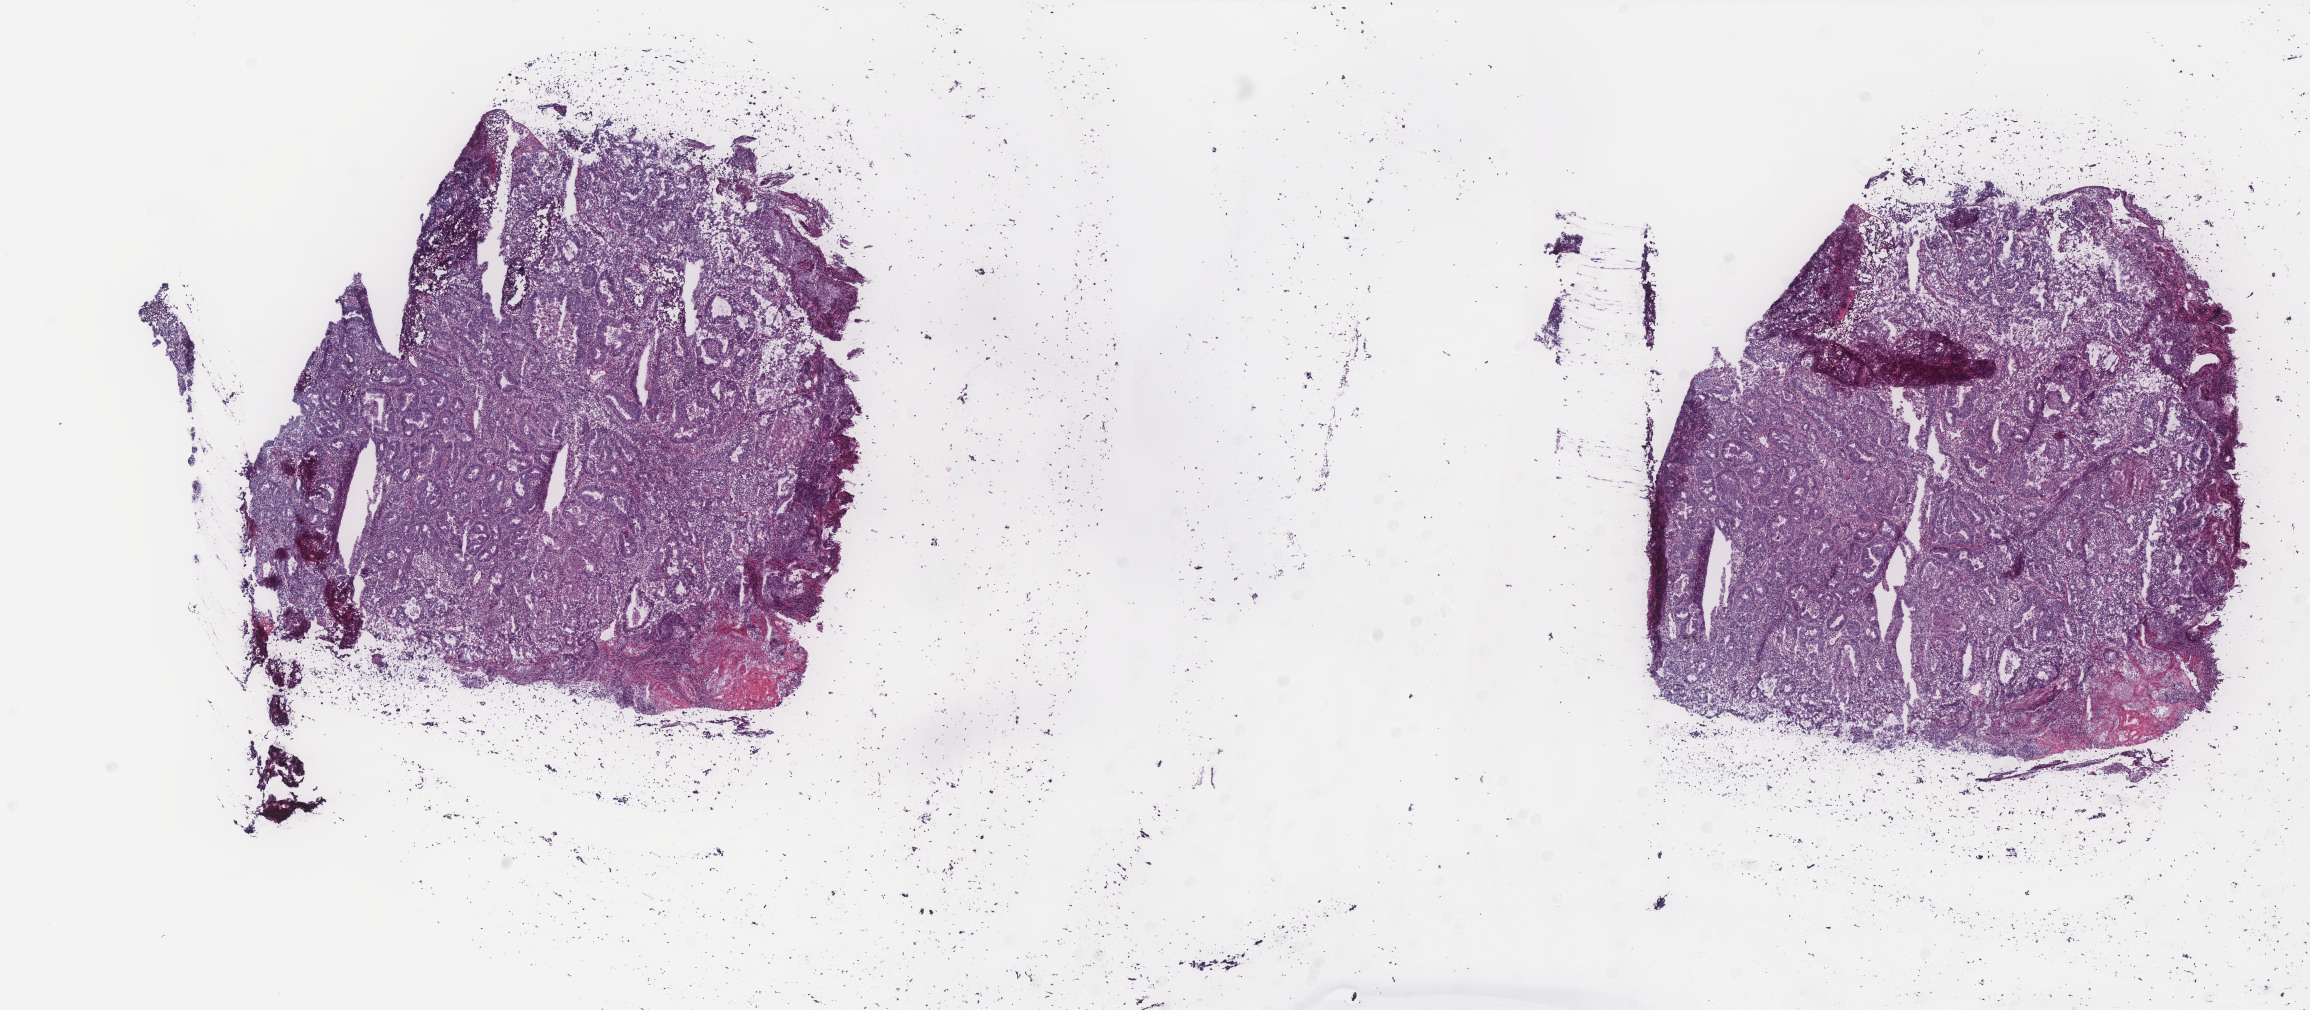
H&E whole-slide image, a low-resolution overview of the entire scanned area, about 18.5 x 8.1 mm (from a 40x scan). Frozen section. Primary tumour sample from the uterus. Female, age 62 years at initial diagnosis. Pathologist review of this section (percent, as recorded): tumour cells 60%, tumour nuclei 70%.
Histologic diagnosis: Endometrioid adenocarcinoma, NOS (endometrium).